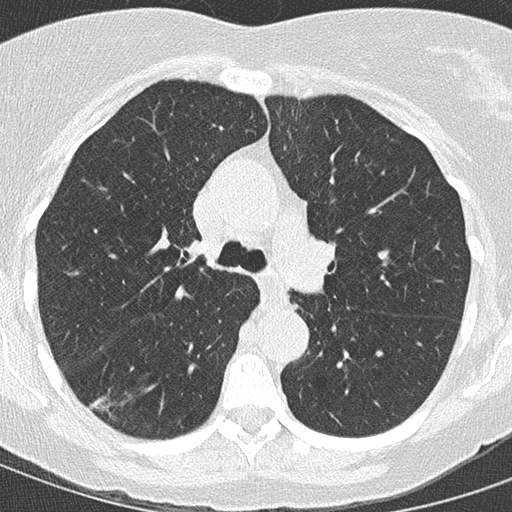
Chest CT (low-dose screening protocol), one axial image; first (baseline) screen; lung window (W 1500 / L -600 HU); 2 mm slice thickness; lung (sharp) reconstruction kernel (B50f); slice 53 of 146 in the series. Female participant, aged 59 years at enrolment. Former smoker at enrolment.
Expert reader's lesion annotation, box from (x=72, y=383) to (x=148, y=441) px. Reader record for this screening exam (exam-level; its link to the box is not recorded): non-calcified nodule or mass ≥4 mm, right lower lobe, 24 × 15 mm, spiculated (stellate) margins, soft tissue attenuation. Official screen result: positive, change unspecified: nodule(s) >= 4 mm or enlarging nodule(s), mass(es), or other non-specific abnormalities suspicious for lung cancer. Lung cancer was diagnosed 12 days after this screen: adenocarcinoma, NOS, right lower lobe, moderately differentiated (G2), stage IIB (AJCC 6th edition), 22 mm at pathology.